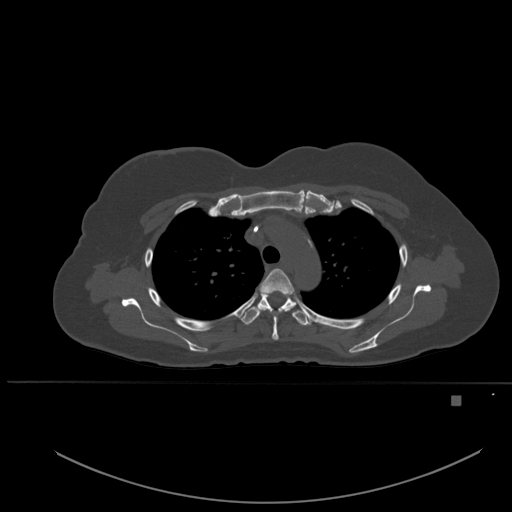
CT including the spine, one axial slice; position 386 of 651 along the scan axis; bone window (W 1800 / L 400 HU); 512 × 512 image matrix, field of view 443 × 443 mm. Patient: female, 49 years. Case-level facts recorded for this patient, not image findings: primary cancer: breast.
Structures marked on this image (semi-automatically segmented with operator editing):
- T3 vertebra: box from (x=260, y=268) to (x=295, y=341) px
- T4 vertebra: (x=240, y=292)–(x=310, y=326)